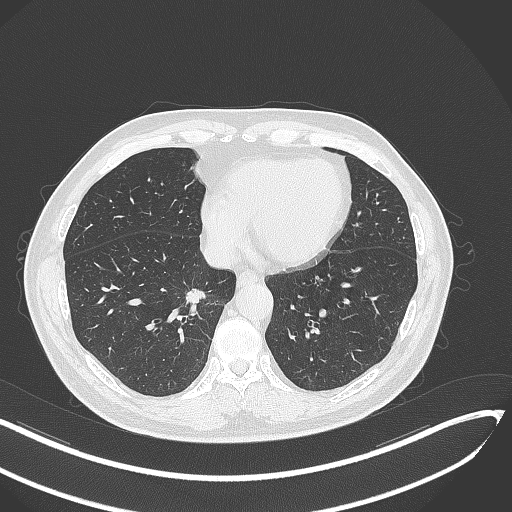
Chest CT, one axial slice; slice 126 of 429 in the series (ordered by position); reconstruction kernel B70f; 120 kVp; lung window (W 1500 / L -600 HU); 512 × 512 image matrix, field of view 400 × 400 mm. Patient: male, 62 years. From the clinical record (not read from this slice): clinical TNM (as recorded): T1b N0 M0; histopathological grade: G2.
Structures marked on this image (rectangle marked by the reading radiologist):
- lung tumour (recorded histology: adenocarcinoma): box from (x=181, y=288) to (x=208, y=318) px